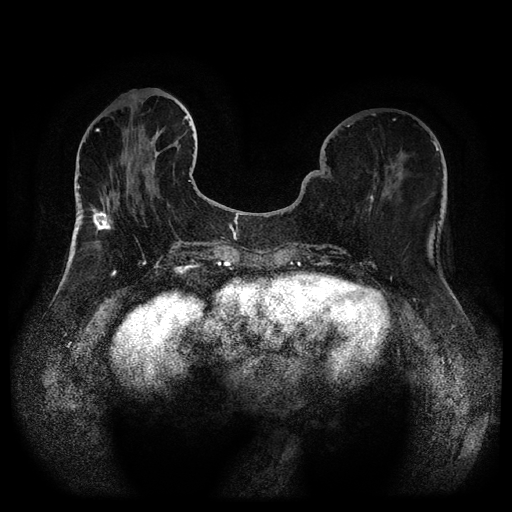
Breast MRI (dynamic contrast-enhanced, multi-phase), one axial slice. Position 34 of 116 along the scan axis. Dynamic contrast-enhanced series, time point 2 of 5 at this slice position (early post-contrast). 1.5 T. TE 2.6 ms, TR 5.3 ms. 2 mm slice thickness. 512 × 512 image matrix. Patient: female, 75 years.
Annotated regions visible in this slice (semi-automatically segmented with operator editing):
- breast lesion (labelled benign in the annotation): bounding box [x1, y1, x2, y2] px = [87, 203, 114, 234]